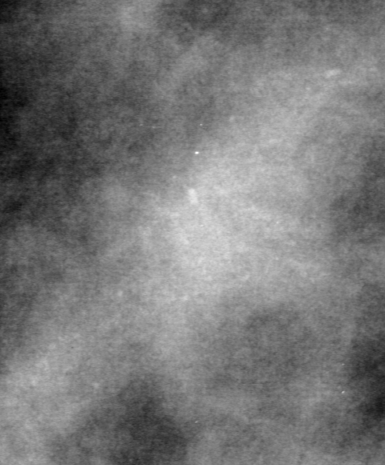
Crop from a digitized film mammogram around one marked abnormality; left breast; MLO view.
Finding: calcifications, morphology pleomorphic, distribution segmental; BI-RADS assessment category 4; subtlety rating 2 on a 1 (subtle) to 5 (obvious) scale; pathology result (as recorded, not read from the image): benign.